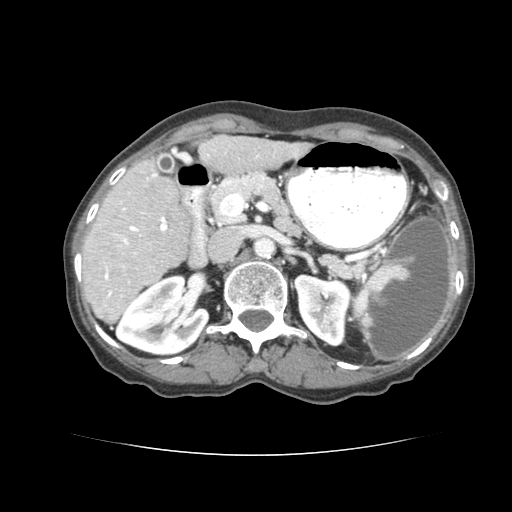
Contrast-enhanced abdominal CT (liver protocol), one axial slice; position 37 of 77 along the scan axis; soft-tissue window (W 400 / L 40 HU); 2.5 mm slice thickness; 512 × 512 image matrix, field of view 340 × 340 mm. From the clinical record (not read from this slice): diagnosis: hepatocellular carcinoma (patient treated with transarterial chemoembolisation; whether this scan precedes or follows treatment is not stated here); TNM stage (as recorded): Stage-I; Child-Pugh class: A; tumour differentiation: well differentiated; tumour nodularity: uninodular.
Outlined on this slice (semi-automatically segmented with operator editing):
- liver parenchyma outside the tumour (the mass and vessels are separate outlines, so this box may not span the whole liver): bounding box (x1, y1, x2, y2) in pixels: (80, 138, 312, 320)
- liver vessels: (96, 155, 274, 305)